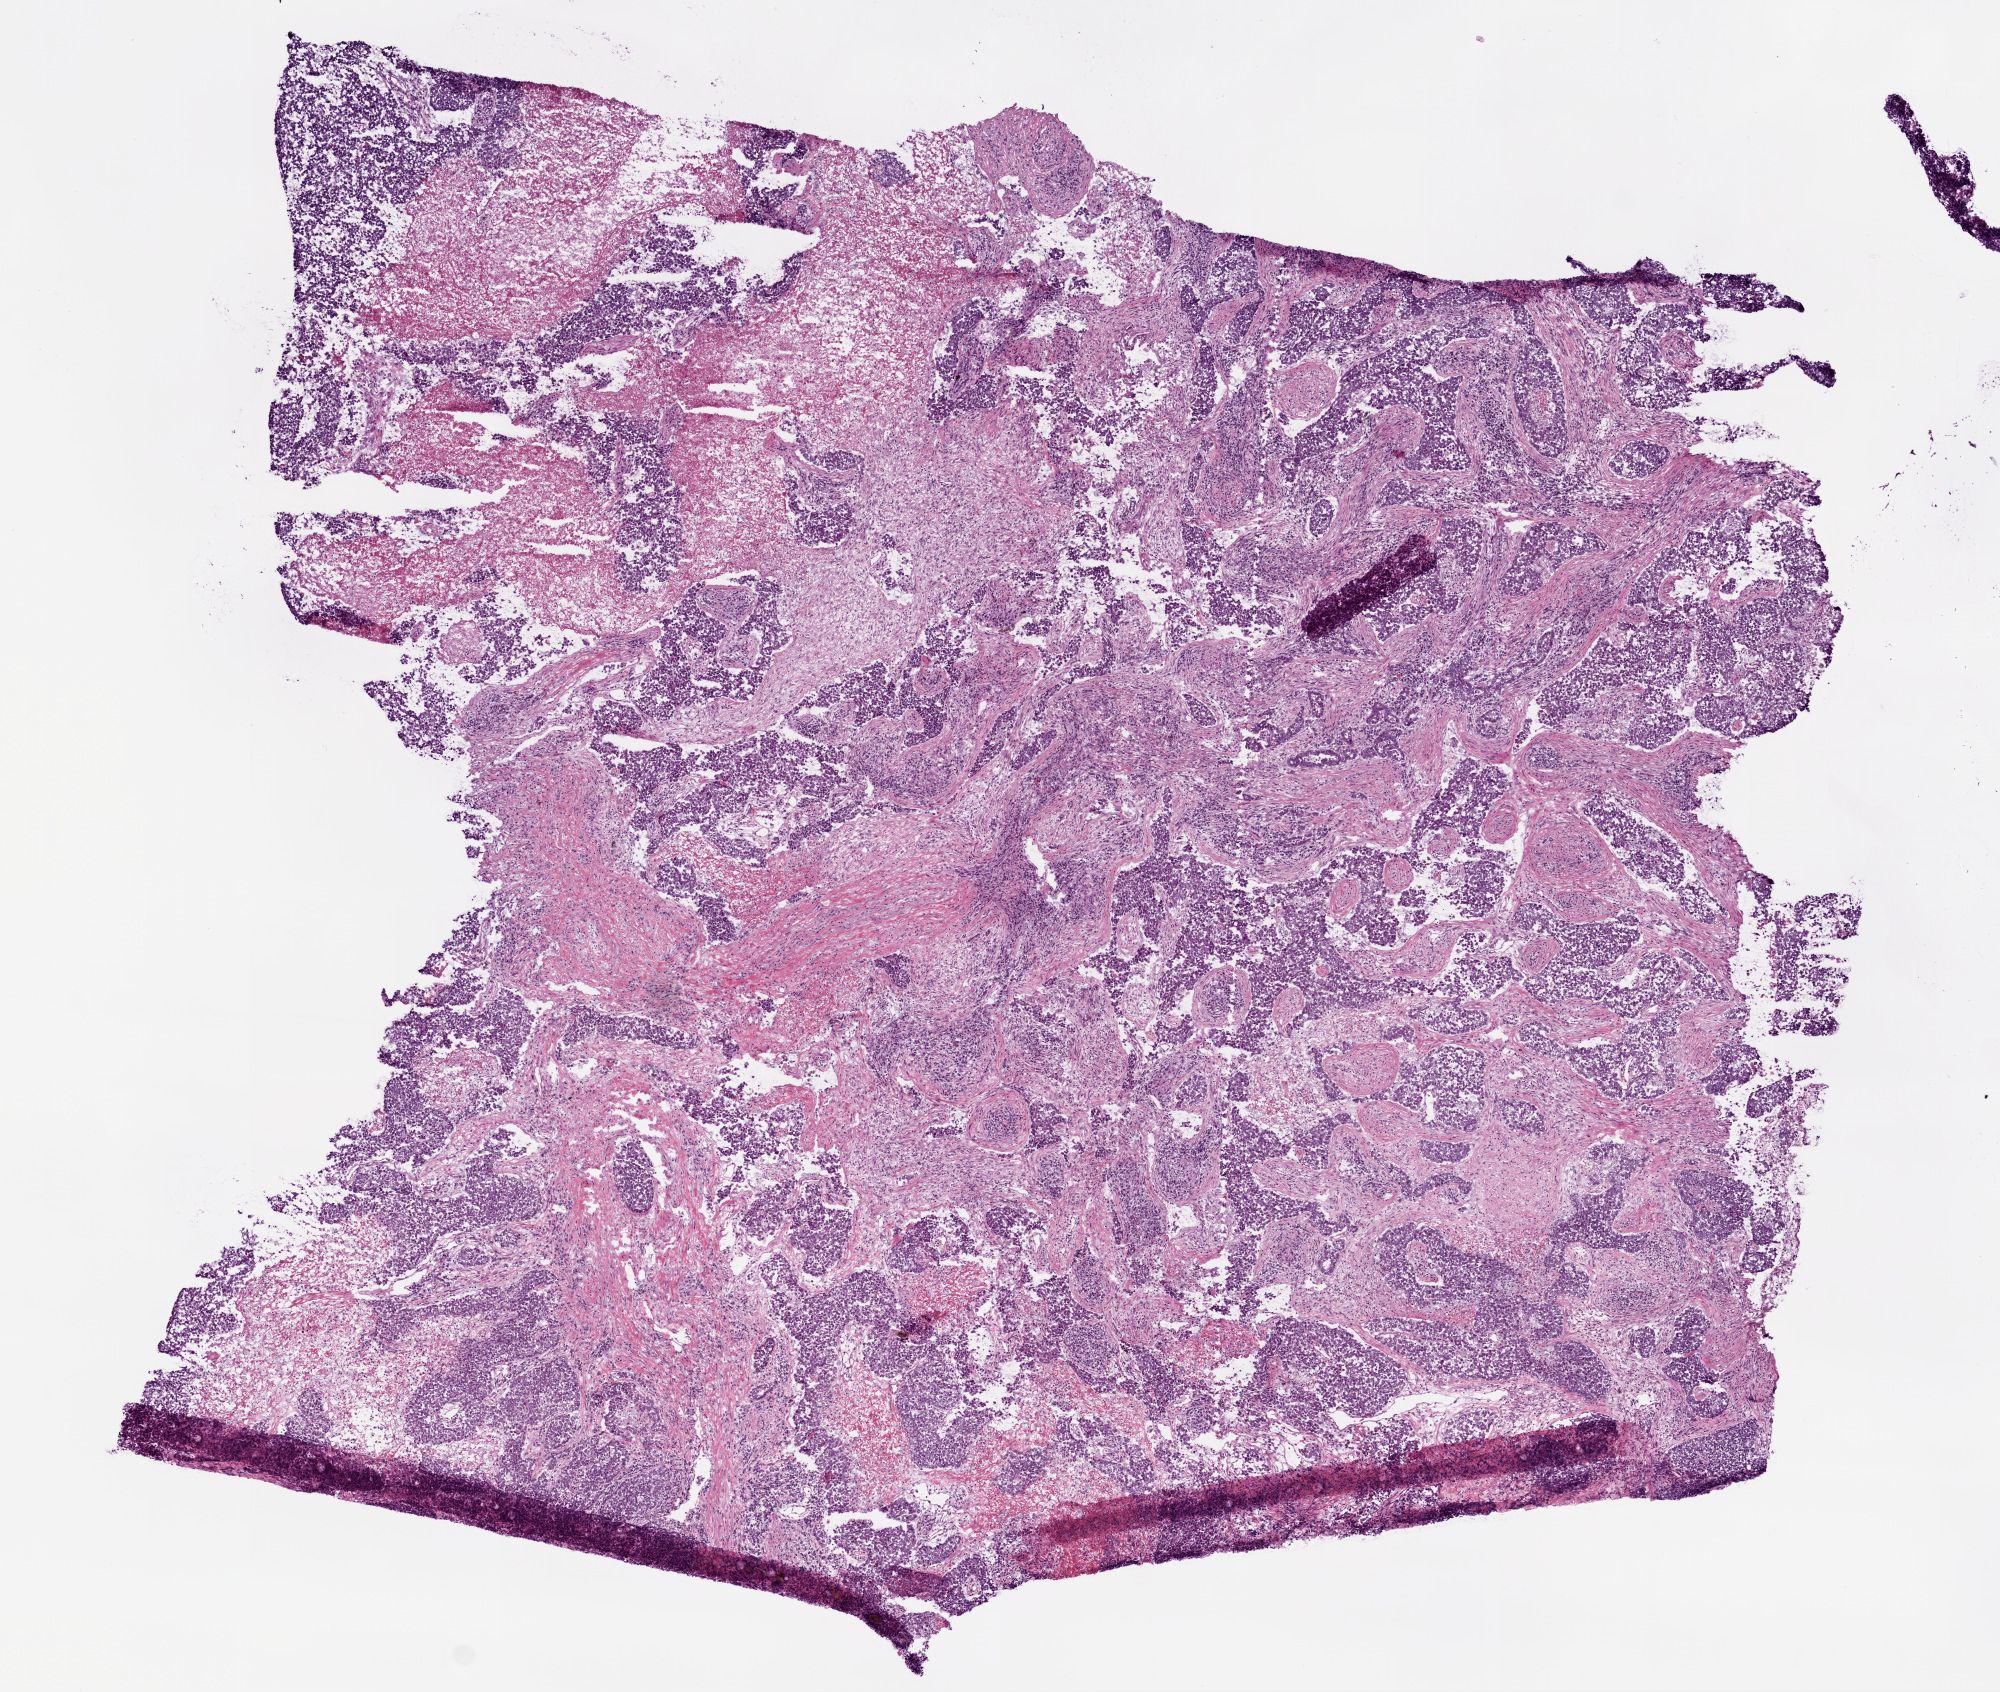
H&E-stained whole-slide image, shown as a low-resolution overview of the whole scanned area (about 8.0 x 6.8 mm), frozen section, primary tumour sample from the lung. Female, age 51 years at initial diagnosis. Pathologist review of this section (percent, as recorded): tumour cells 65%, tumour nuclei 80%, normal cells 0%, stromal cells 35%, necrosis 10%.
Diagnosis: Adenocarcinoma, NOS. AJCC pathologic stage: IB (7th edition).